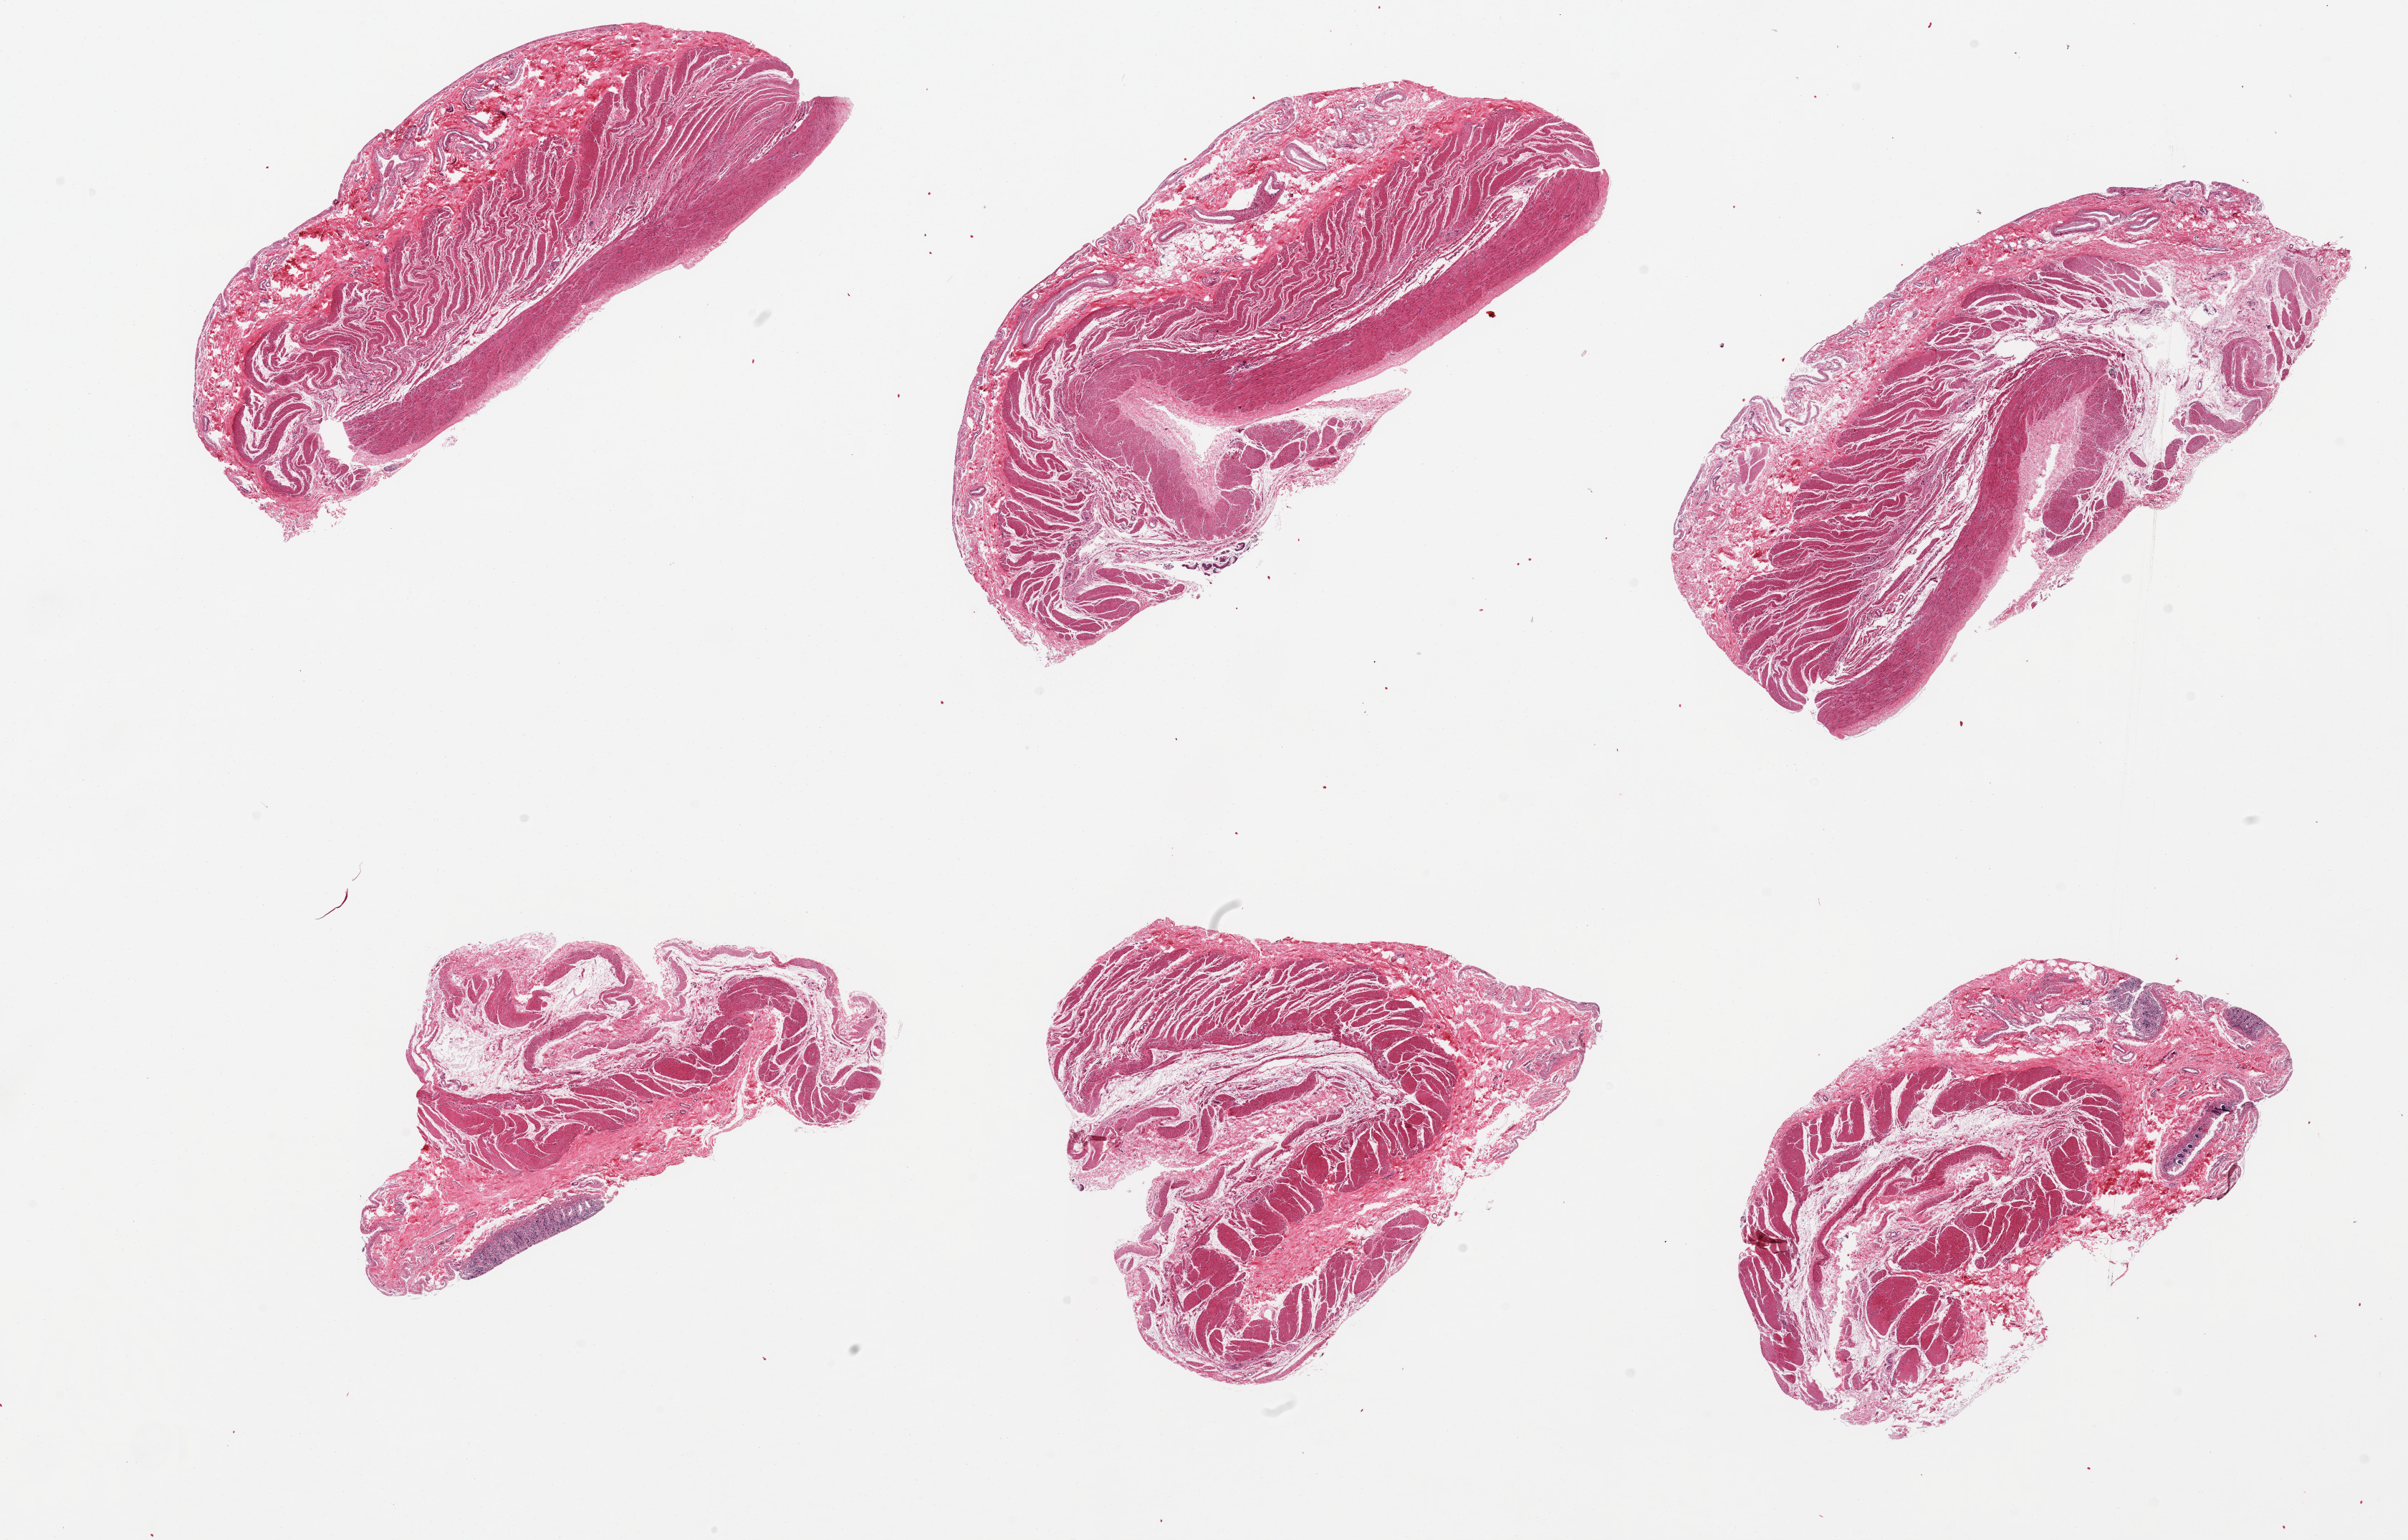
Whole-slide image, haematoxylin and eosin stain — whole scanned area (about 26.6 x 17.0 mm, acquisition: 20x scan) shown as a low-resolution overview, PAXgene-fixed, paraffin-embedded tissue, section of sigmoid colon (target tissue), donor tissue sample. Donor sex: female.
• reviewer comment on this tissue sample: 6 pieces; 2 (from 1 aliquot) have extraneous mucosa & submucosa